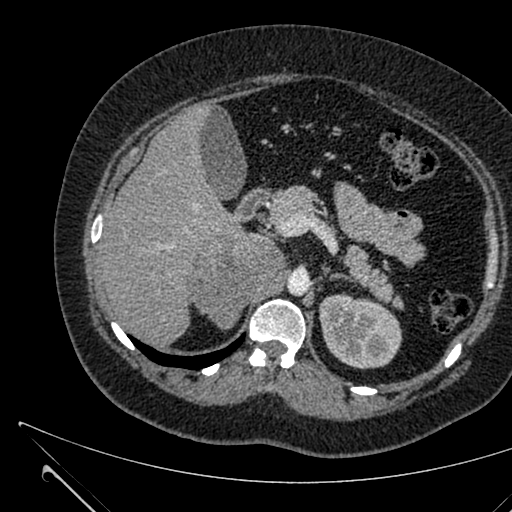
Contrast-enhanced abdominal CT, one axial slice; position 423 of 731 along the scan axis; 120 kVp; intravenous contrast given; soft-tissue window (W 400 / L 40 HU); 512 × 512 image matrix. Patient: female, 36 years. Case-level facts recorded for this patient, not image findings: diagnosis: adrenocortical carcinoma; tumour side: right adrenal; tumour size at pathology: 10 cm; Ki-67 index: 20 %; stage (as recorded): 4.
Annotated regions visible in this slice (semi-automatically segmented with operator editing):
- mass: box from (x=191, y=234) to (x=285, y=329) px